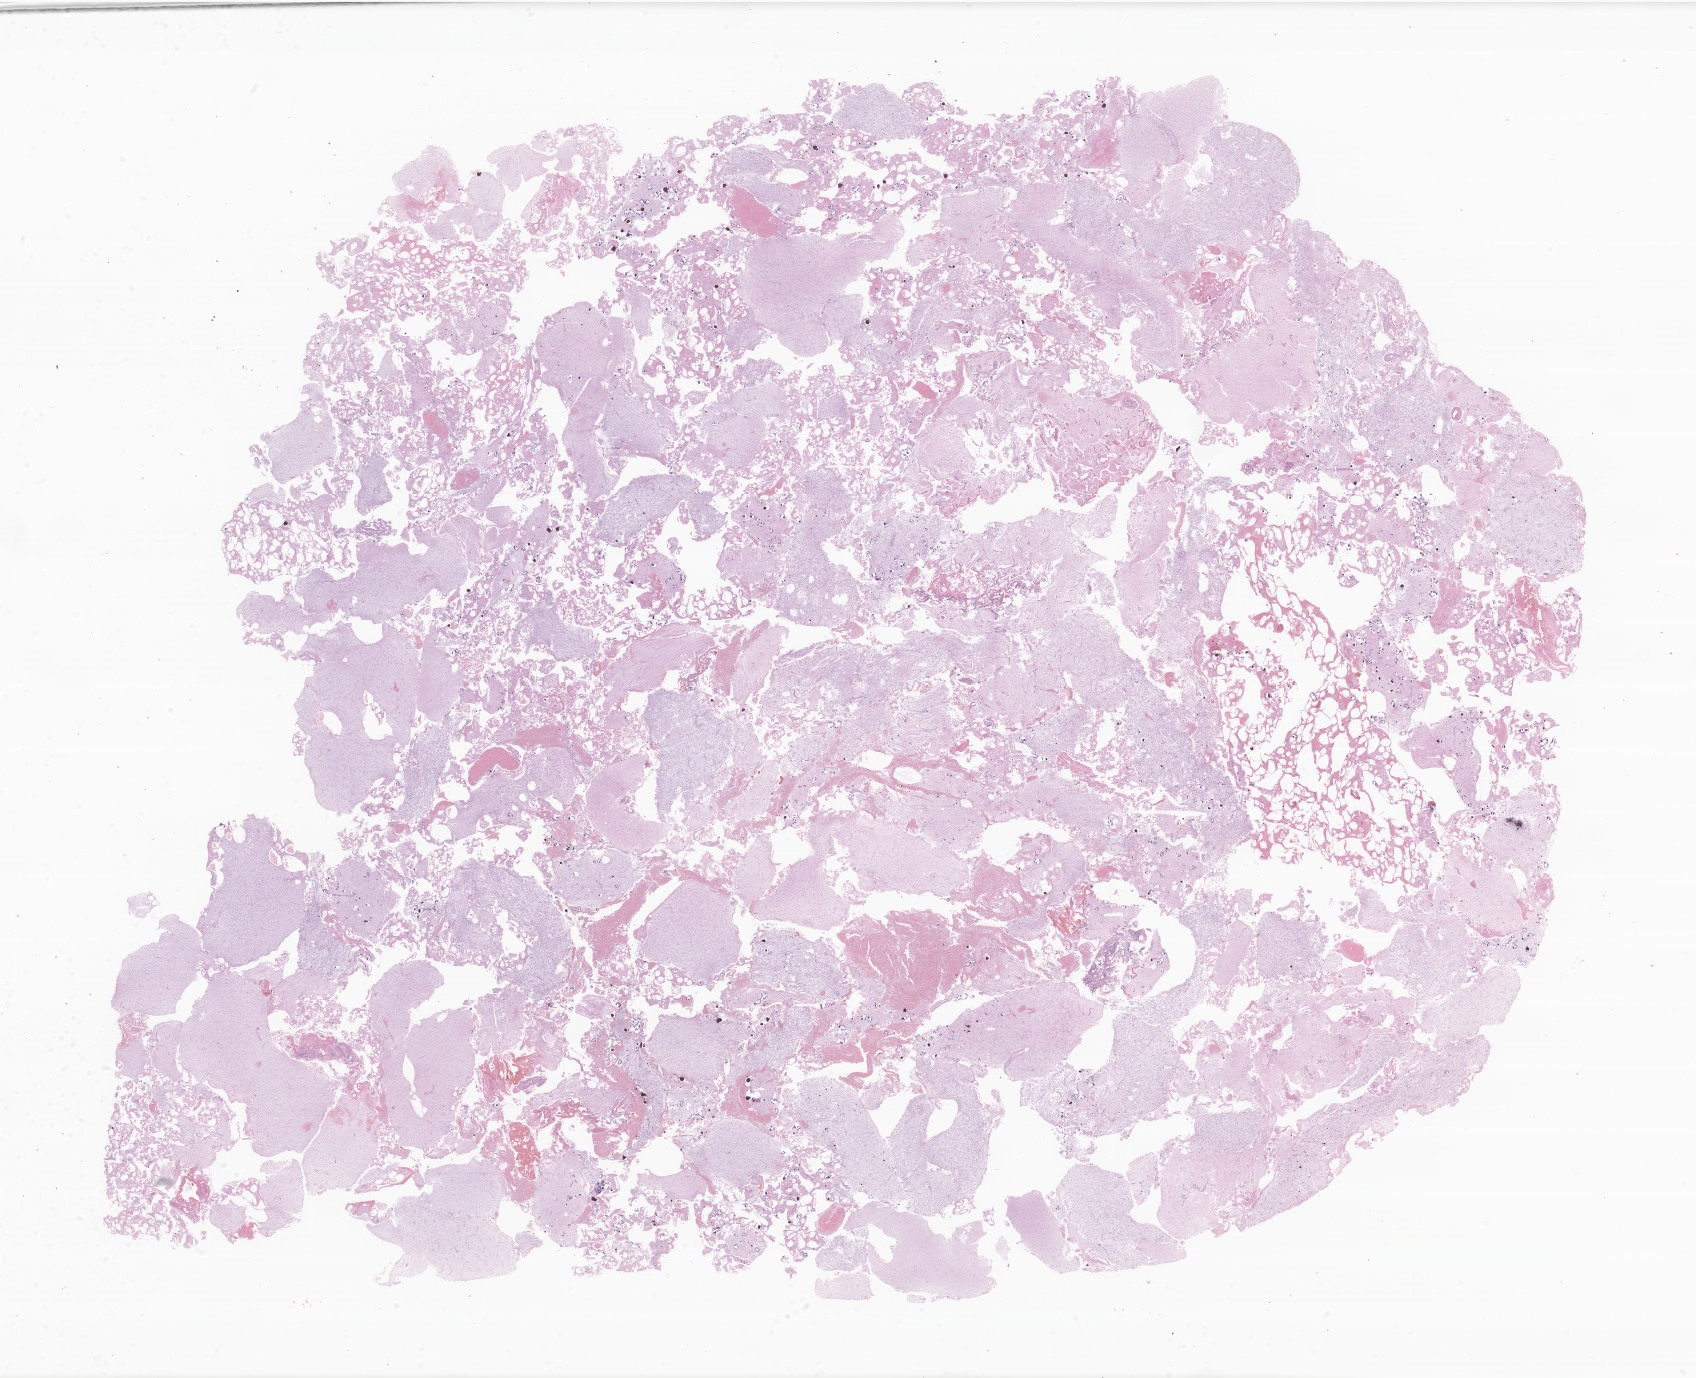
Hematoxylin and eosin (H&E) whole-slide image of tumor tissue from the brain, shown as a low-resolution overview of the whole scanned area (about 28.6 x 23.2 mm); formalin-fixed paraffin-embedded section. Patient: male, age 197 months (16 years 5 months).
Diagnosis: Neoplasm, uncertain whether benign or malignant.